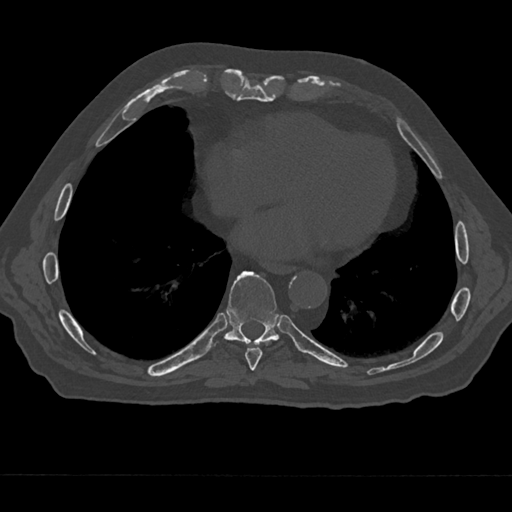
CT including the spine, one axial slice; position 285 of 797 along the scan axis; 120 kVp; bone window (W 1800 / L 400 HU); 0.5 mm slice thickness; 512 × 512 image matrix. Male patient, age 75 years. Case-level facts recorded for this patient, not image findings: primary cancer: renal.
Annotated regions visible in this slice (semi-automatically segmented with operator editing):
- T8 vertebra: box from (x=245, y=342) to (x=269, y=371) px
- T9 vertebra: (x=212, y=271)–(x=290, y=354)